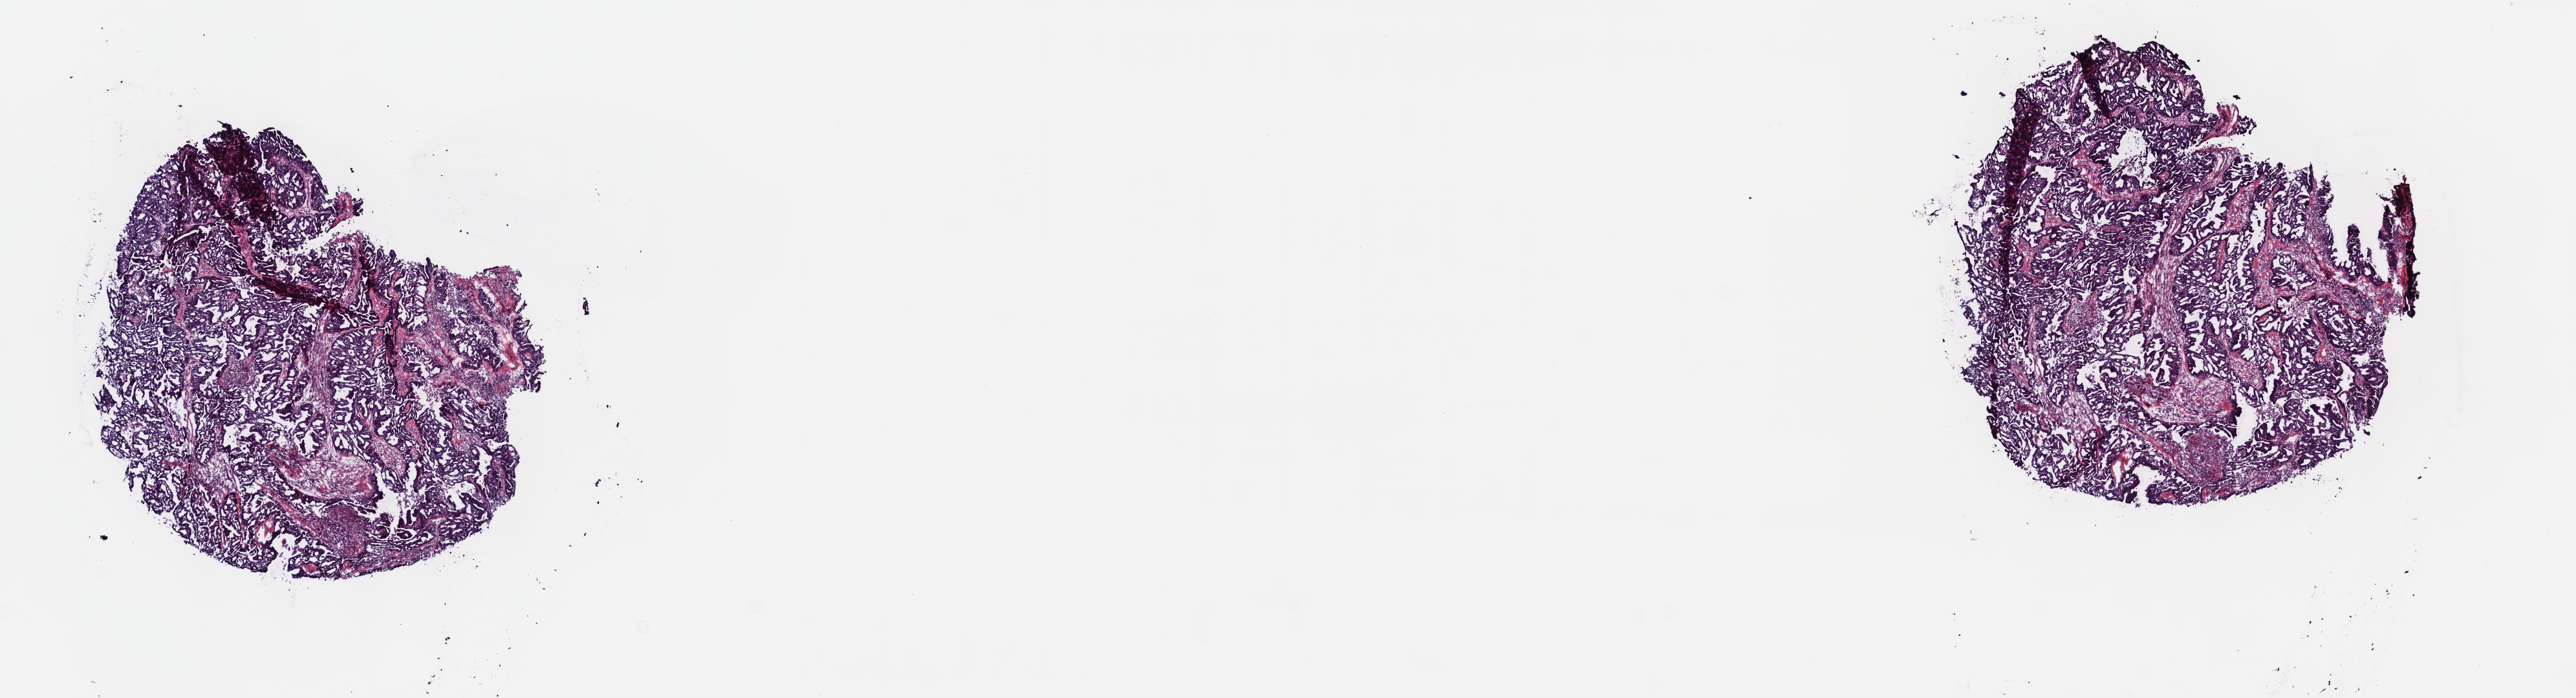
Digitized H&E-stained tissue section (whole slide) — low-resolution overview of the scanned area, about 16.1 x 4.4 mm. Frozen section. Sample: primary tumour, ovary. Female patient; age at initial diagnosis 55 years. Histologic grade: G3 (poorly differentiated). Slide review estimates, as recorded: tumour cells 80%, tumour nuclei 80%, normal cells 5%, stromal cells 15%, necrosis 0%. Infiltration values recorded for this section: lymphocyte infiltration 5%, monocyte infiltration 0%, neutrophil infiltration 0%.
* FIGO stage: IIB
* histologic diagnosis: Cystadenocarcinoma, NOS